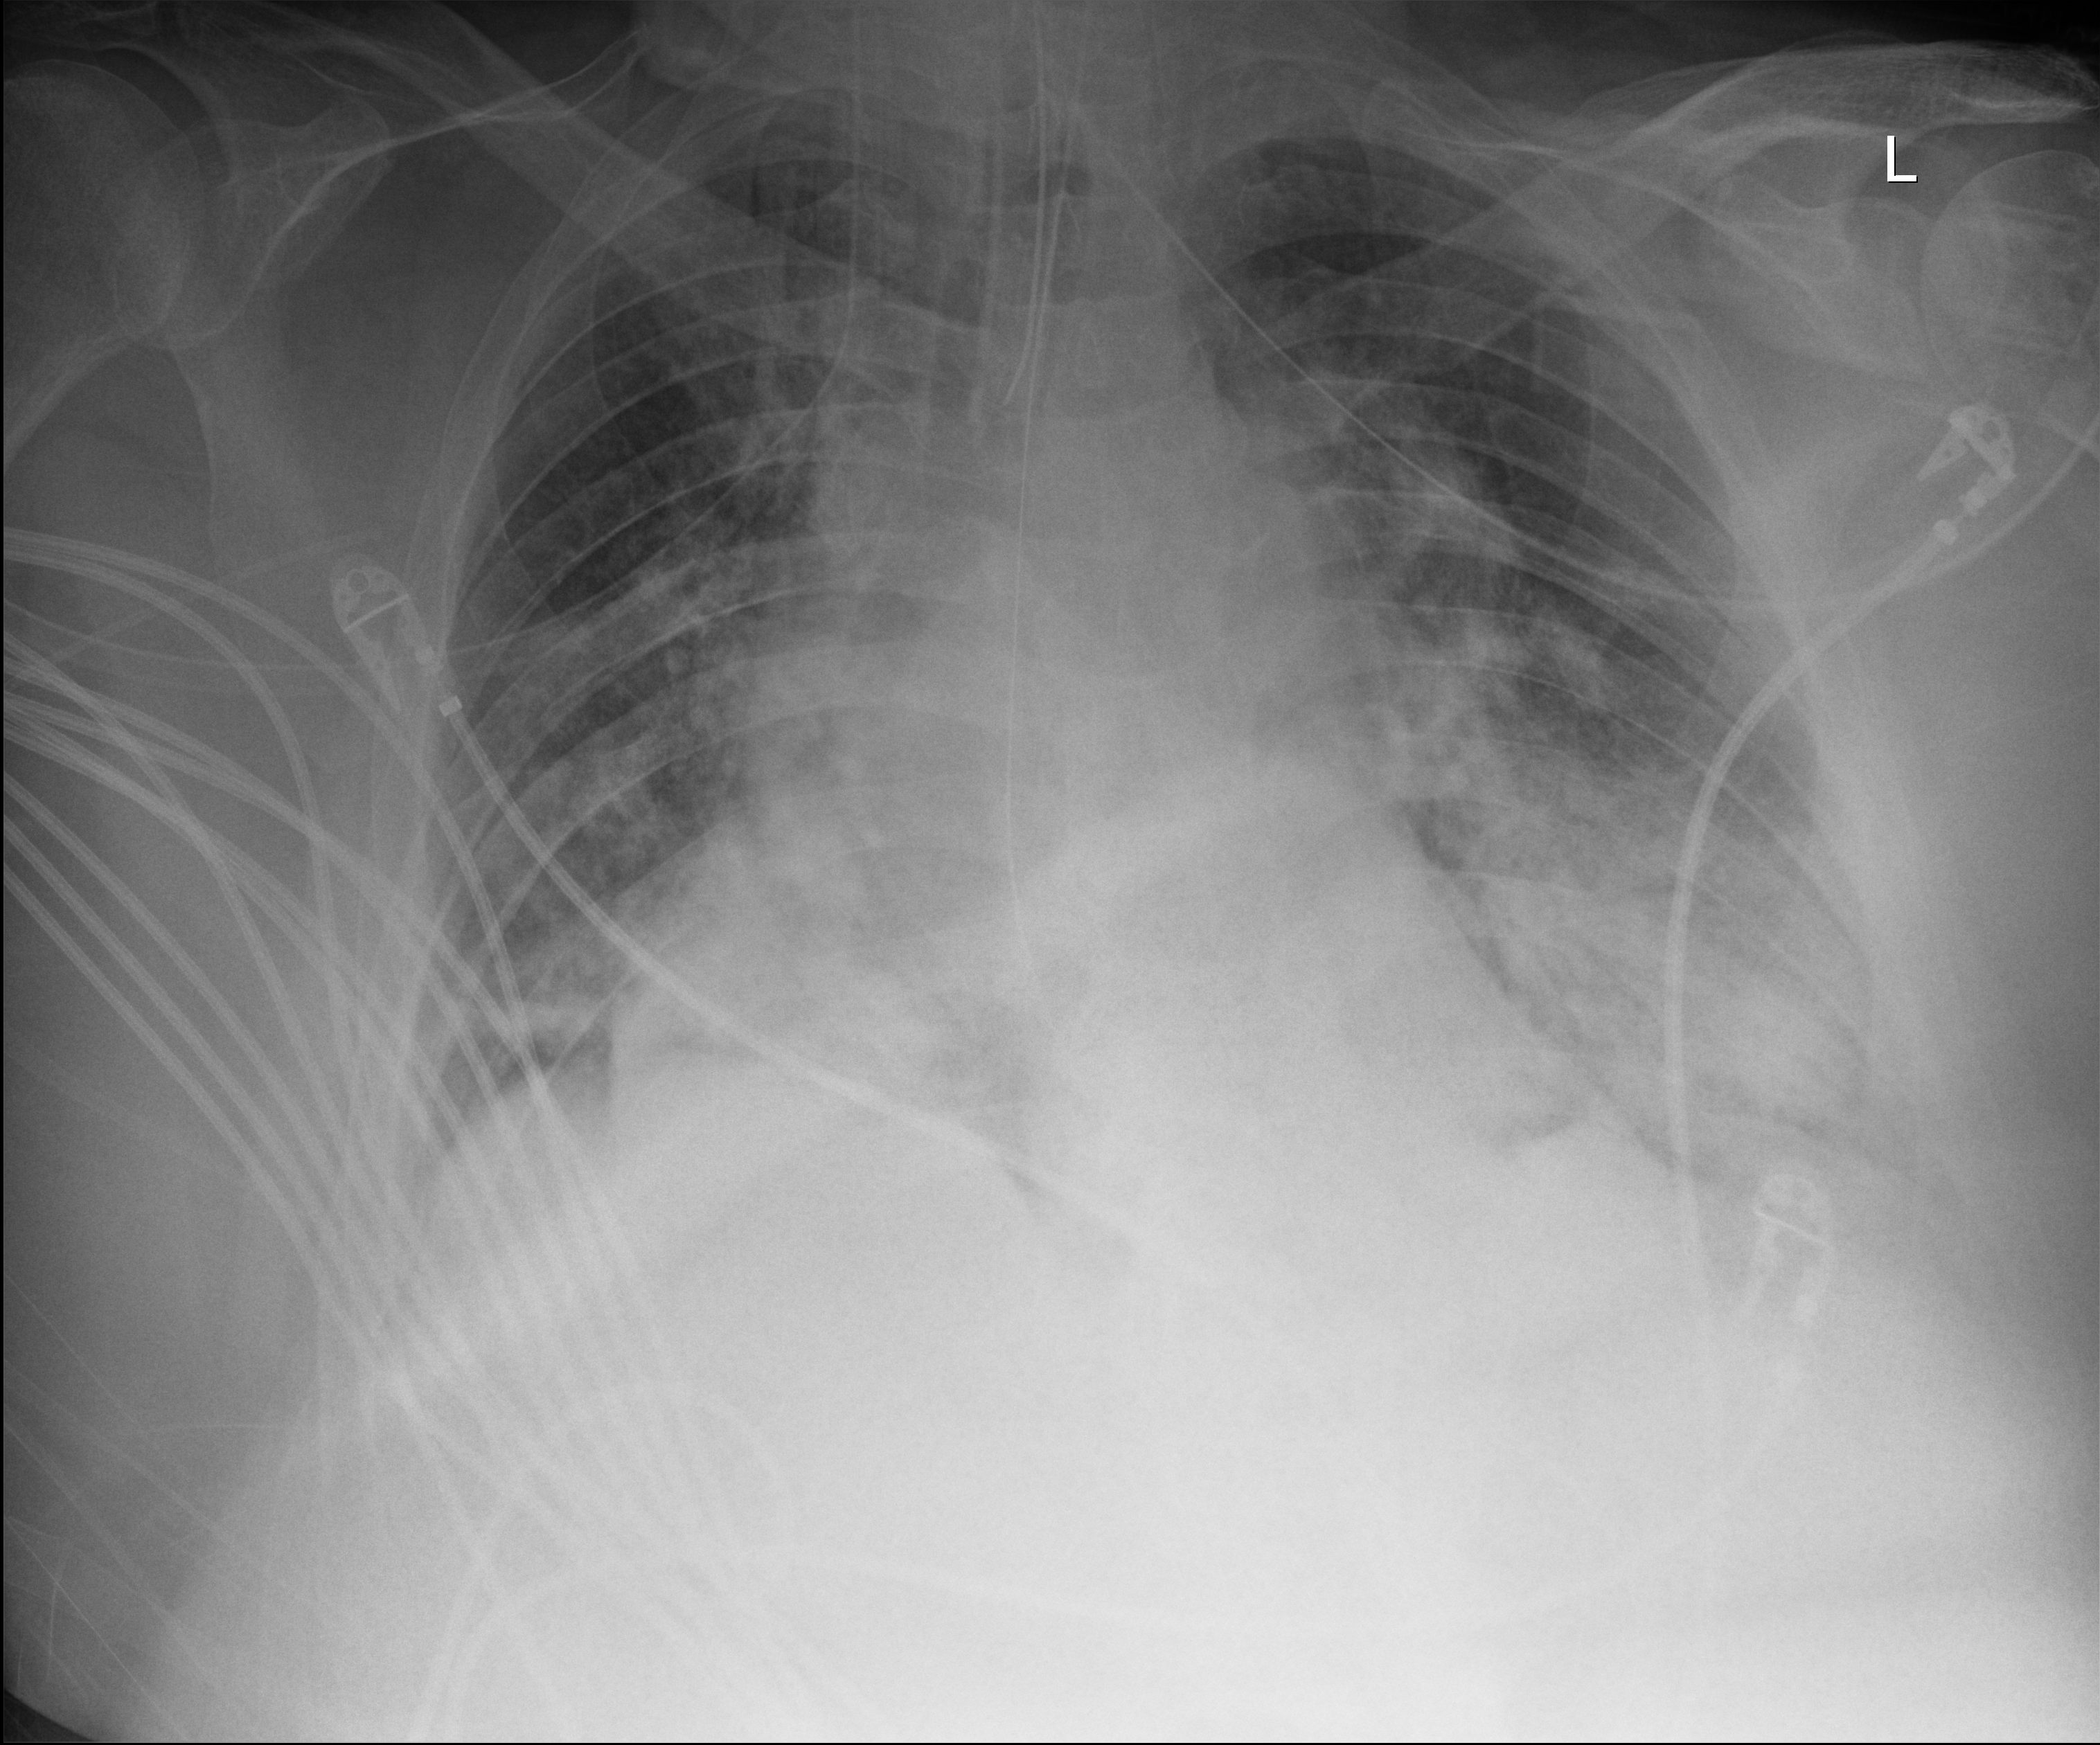
Chest X-ray; anteroposterior (AP) projection. Male patient hospitalised with COVID-19, age 60–74 years.
From the hospital-stay record, not from the radiograph (when in the stay this image was taken is not recorded): mechanically ventilated during this hospital stay: yes.